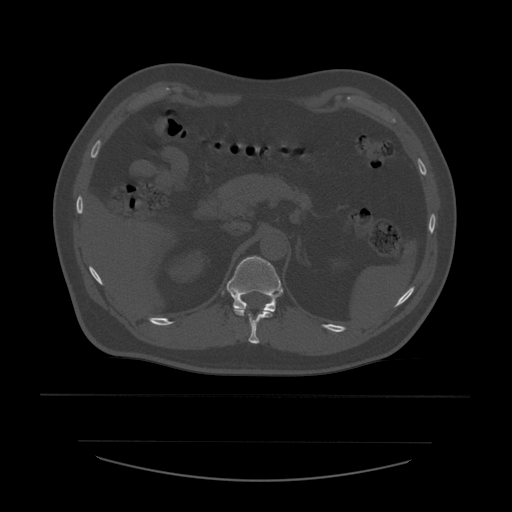
CT including the spine, one axial slice; slice 261 of 532 in the series (ordered by position); bone window (W 1800 / L 400 HU); 1.25 mm slice thickness; 512 × 512 image matrix, field of view 441 × 441 mm. Patient age 44 years. From the clinical record (not read from this slice): primary cancer: soft tissue sarcoma.
Structures marked on this image (semi-automatically segmented with operator editing):
- T11 vertebra: box from (x=233, y=296) to (x=275, y=344) px
- T12 vertebra: (x=227, y=256)–(x=283, y=312)